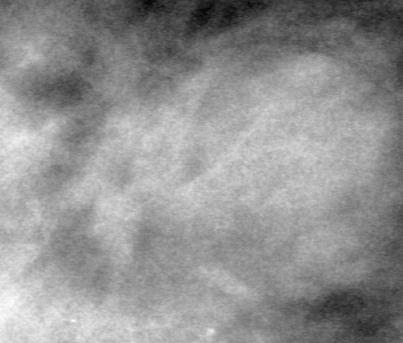
Crop from a digitized film mammogram around one marked abnormality; left breast; MLO view; BI-RADS breast density category 4 (scale 1–4).
Finding: mass, shape round, margins circumscribed; BI-RADS assessment category 4; pathology (as recorded): benign.